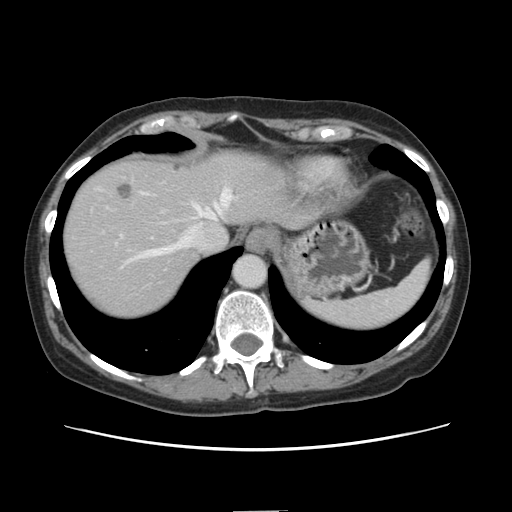
Contrast-enhanced abdominal CT, one axial slice. Position 119 of 141 along the scan axis. 120 kVp. Intravenous contrast given. Soft-tissue window (W 400 / L 40 HU). 2.5 mm slice thickness. 512 × 512 image matrix, field of view 350 × 350 mm. Female patient, age 63 years. Case-level facts recorded for this patient, not image findings: diagnosis: colorectal cancer liver metastases, imaged before liver resection; multiple liver metastases: yes; largest metastasis: 3.2 cm.
Structures marked on this image (manually delineated by an expert):
- hepatic veins: bounding box <134,189,231,259> (left, top, right, bottom; pixels)
- liver: <63,152,297,320>
- planned liver remnant (the part of the liver to remain after resection): <202,152,302,227>
- portal vein (with intrahepatic branches): <143,193,219,204>